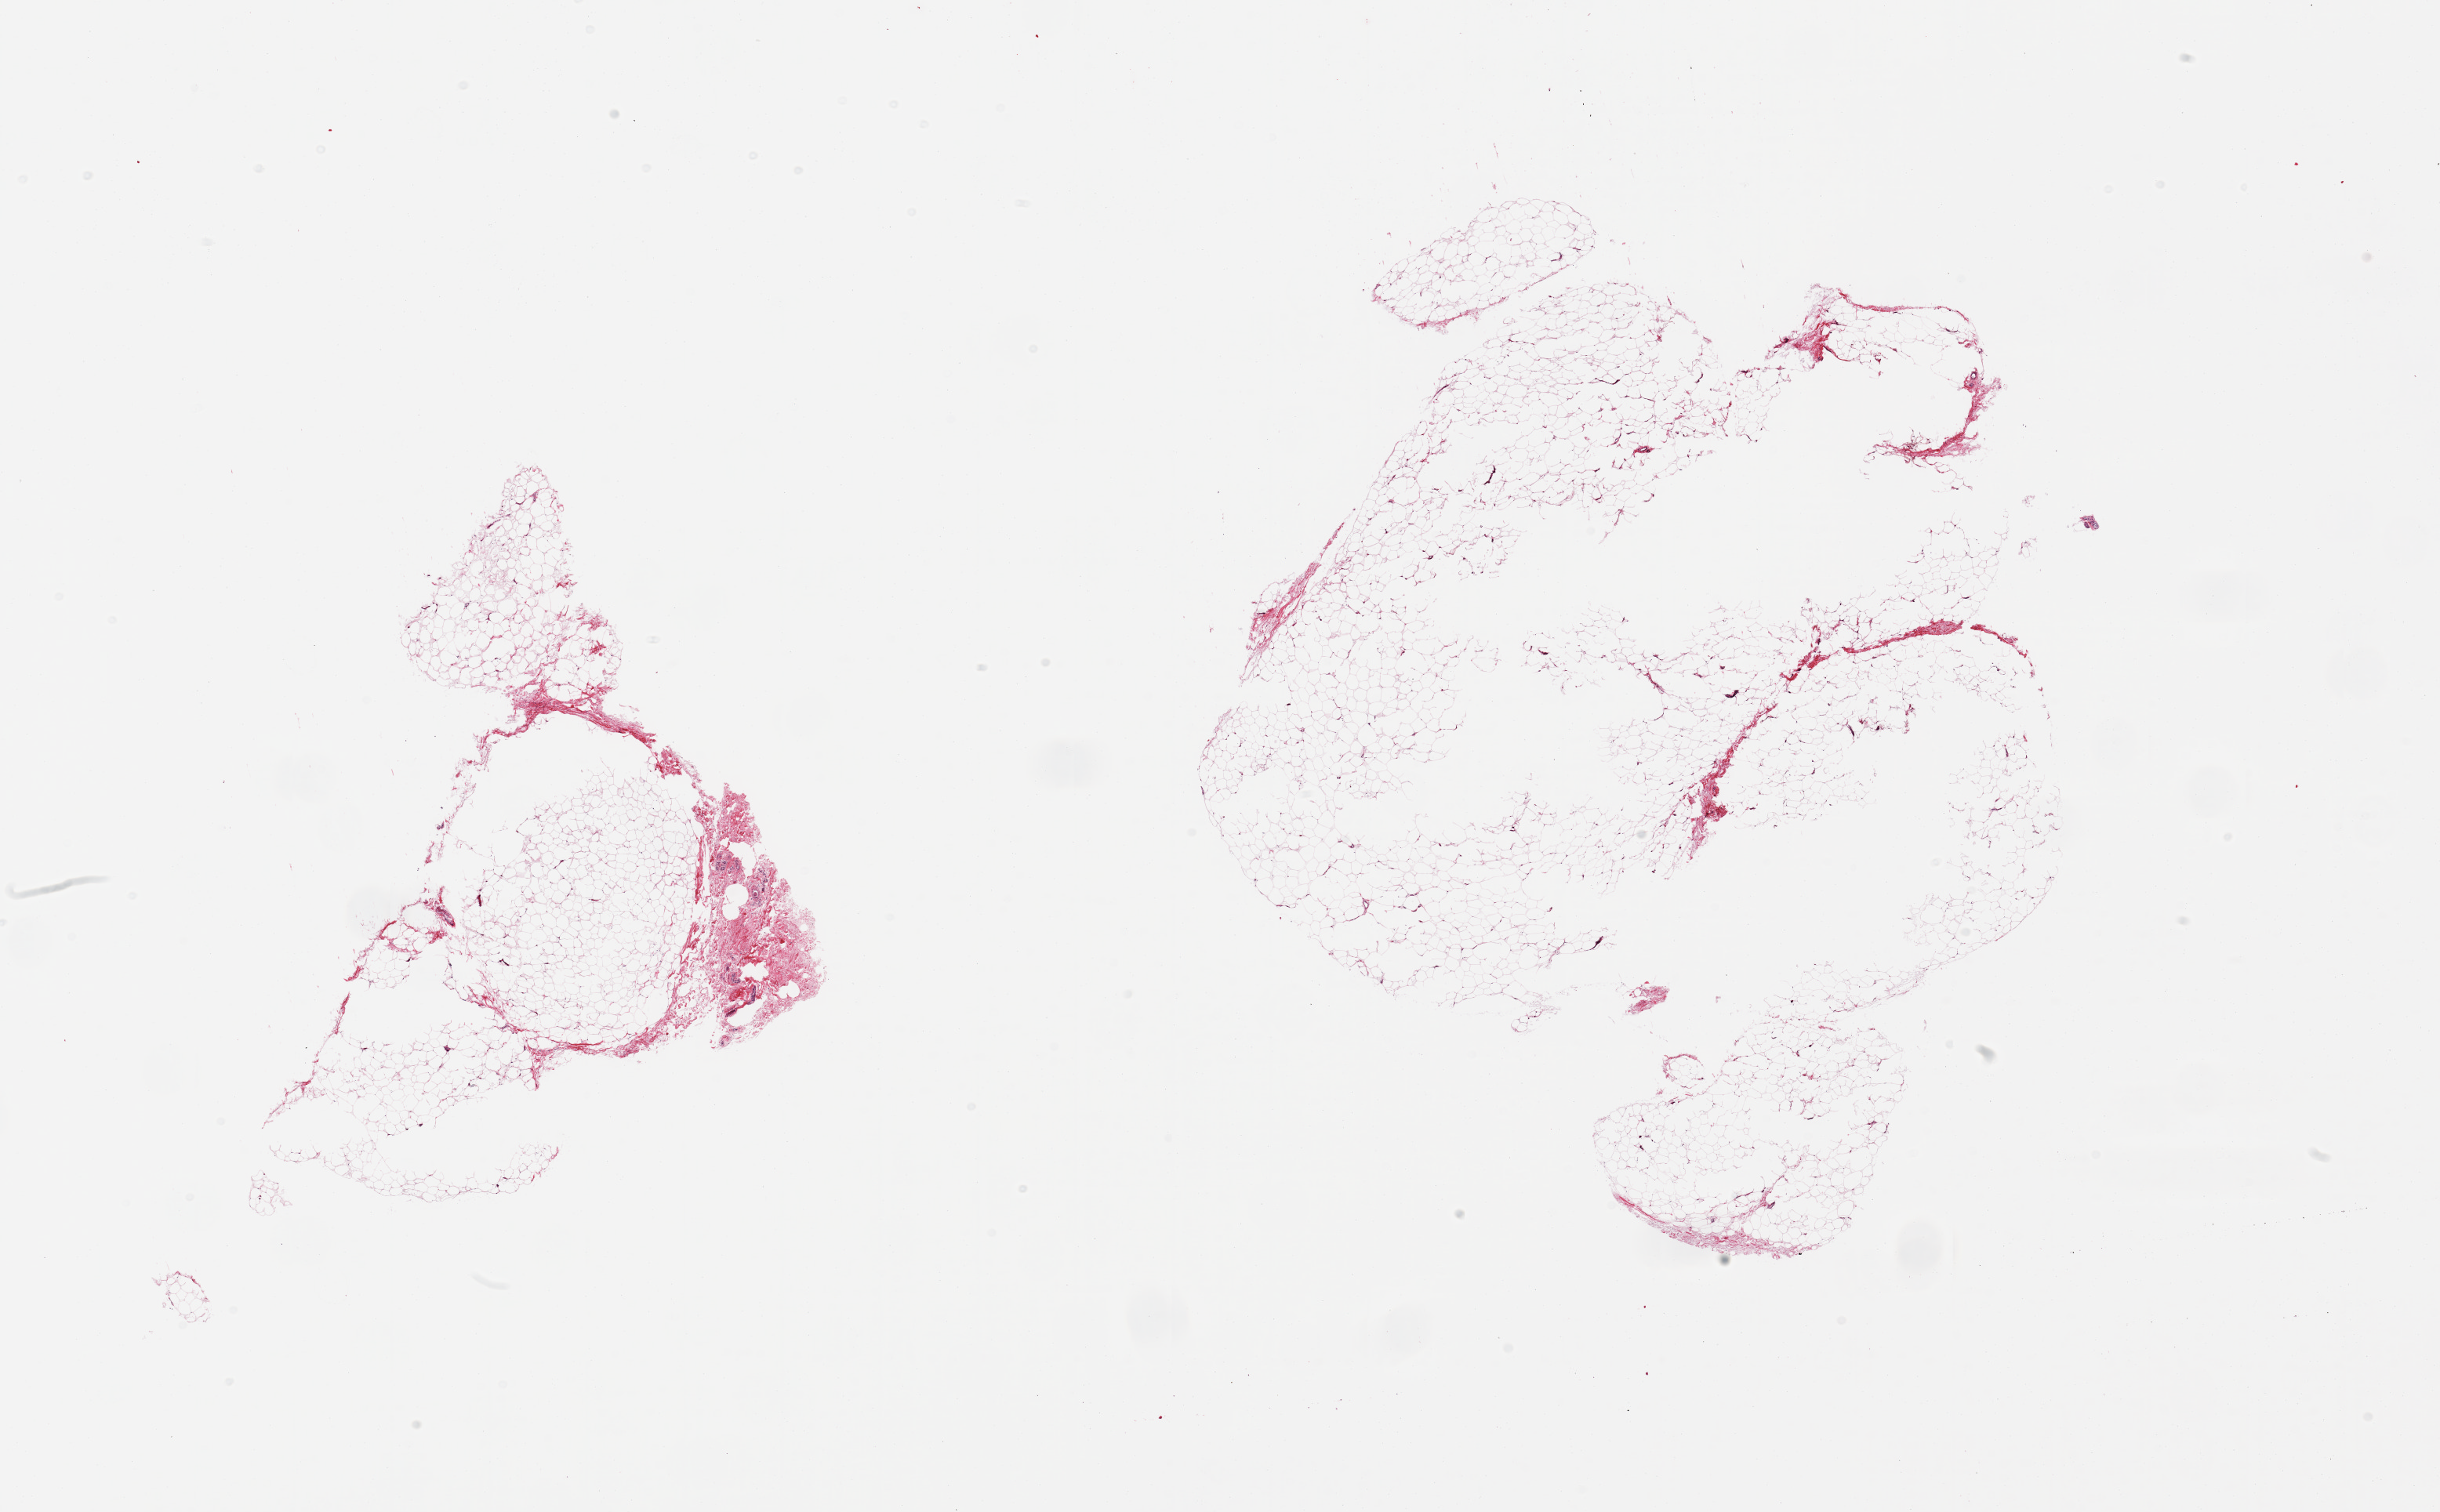
Whole-slide image, haematoxylin and eosin stain — low-resolution overview of the scanned area, about 24.6 x 15.3 mm; PAXgene-fixed, paraffin-embedded tissue; section of adipose tissue (target tissue); donor tissue sample. Donor: male.
Reviewer comment on this tissue sample: 2 pieces; large central defects (? poor fixation), smaller piece includes ~10-20% fibrous tissue.